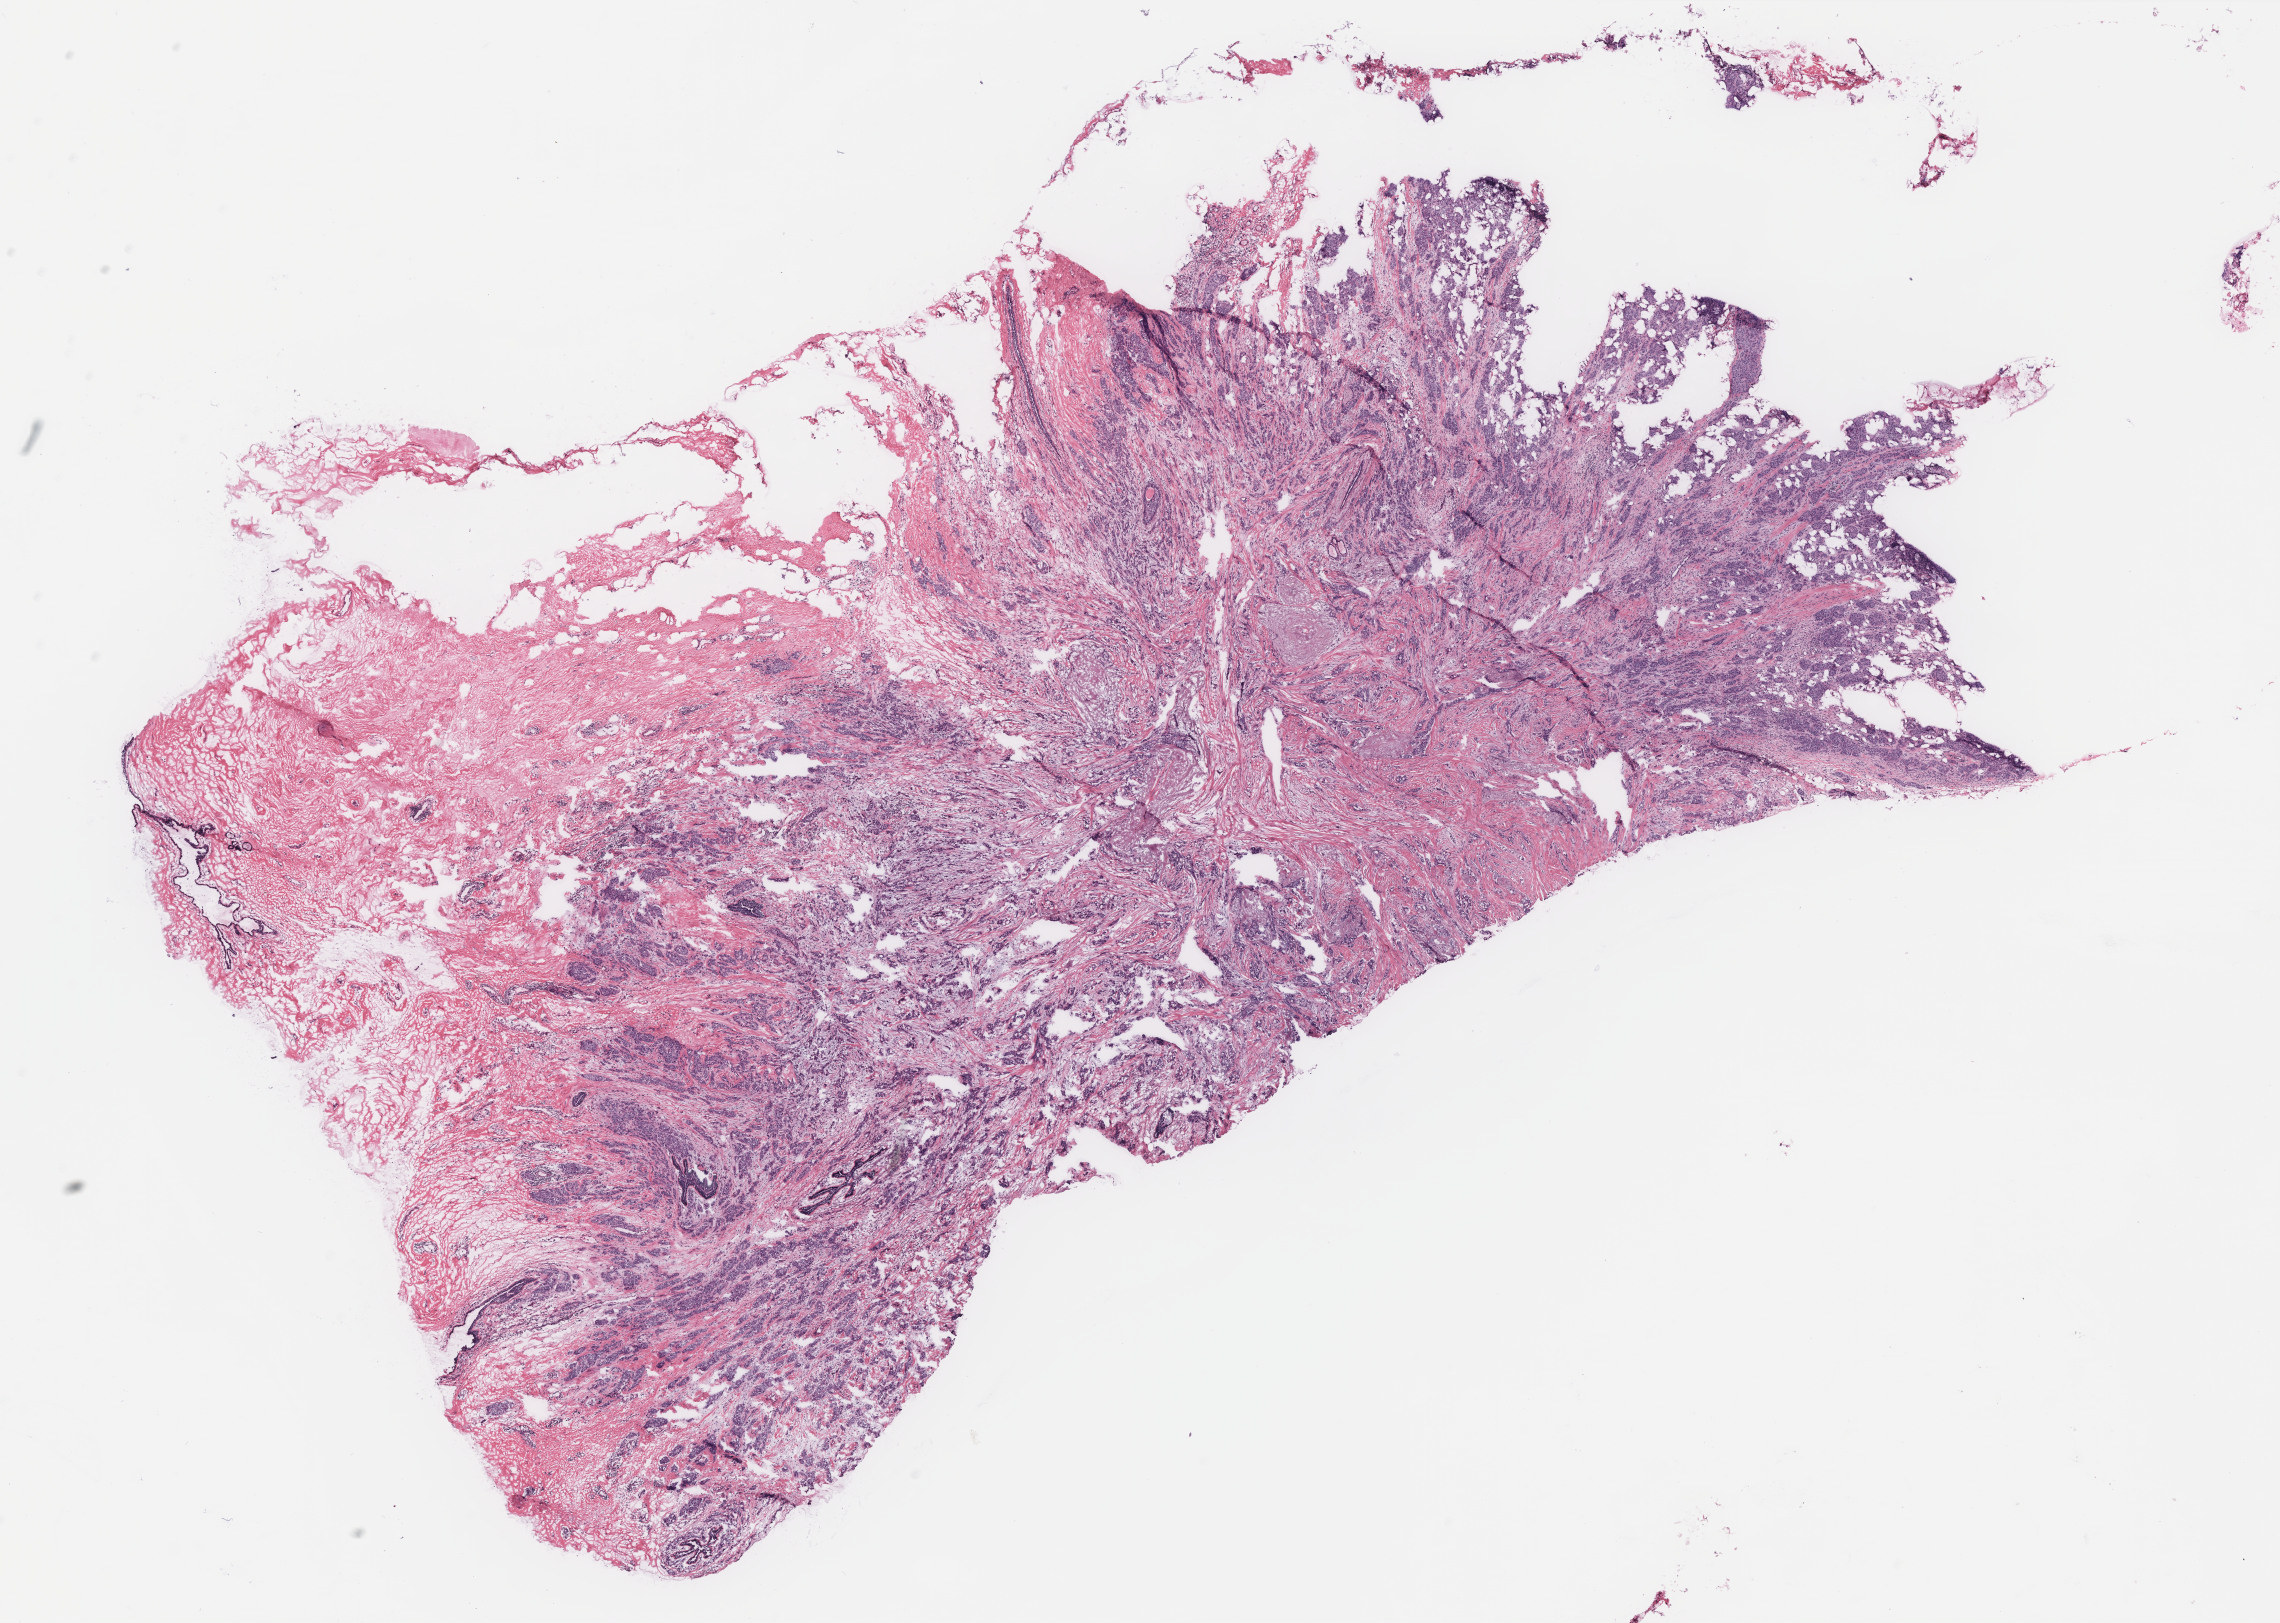
Whole-slide histology image, Hematoxylin and eosin (H&E) stained — a low-resolution overview of the entire scanned area, about 18.2 x 13.0 mm (slide scanned at 40x), breast, tissue type not recorded.
Patient diagnosis (cohort enrolment): breast cancer (breast).